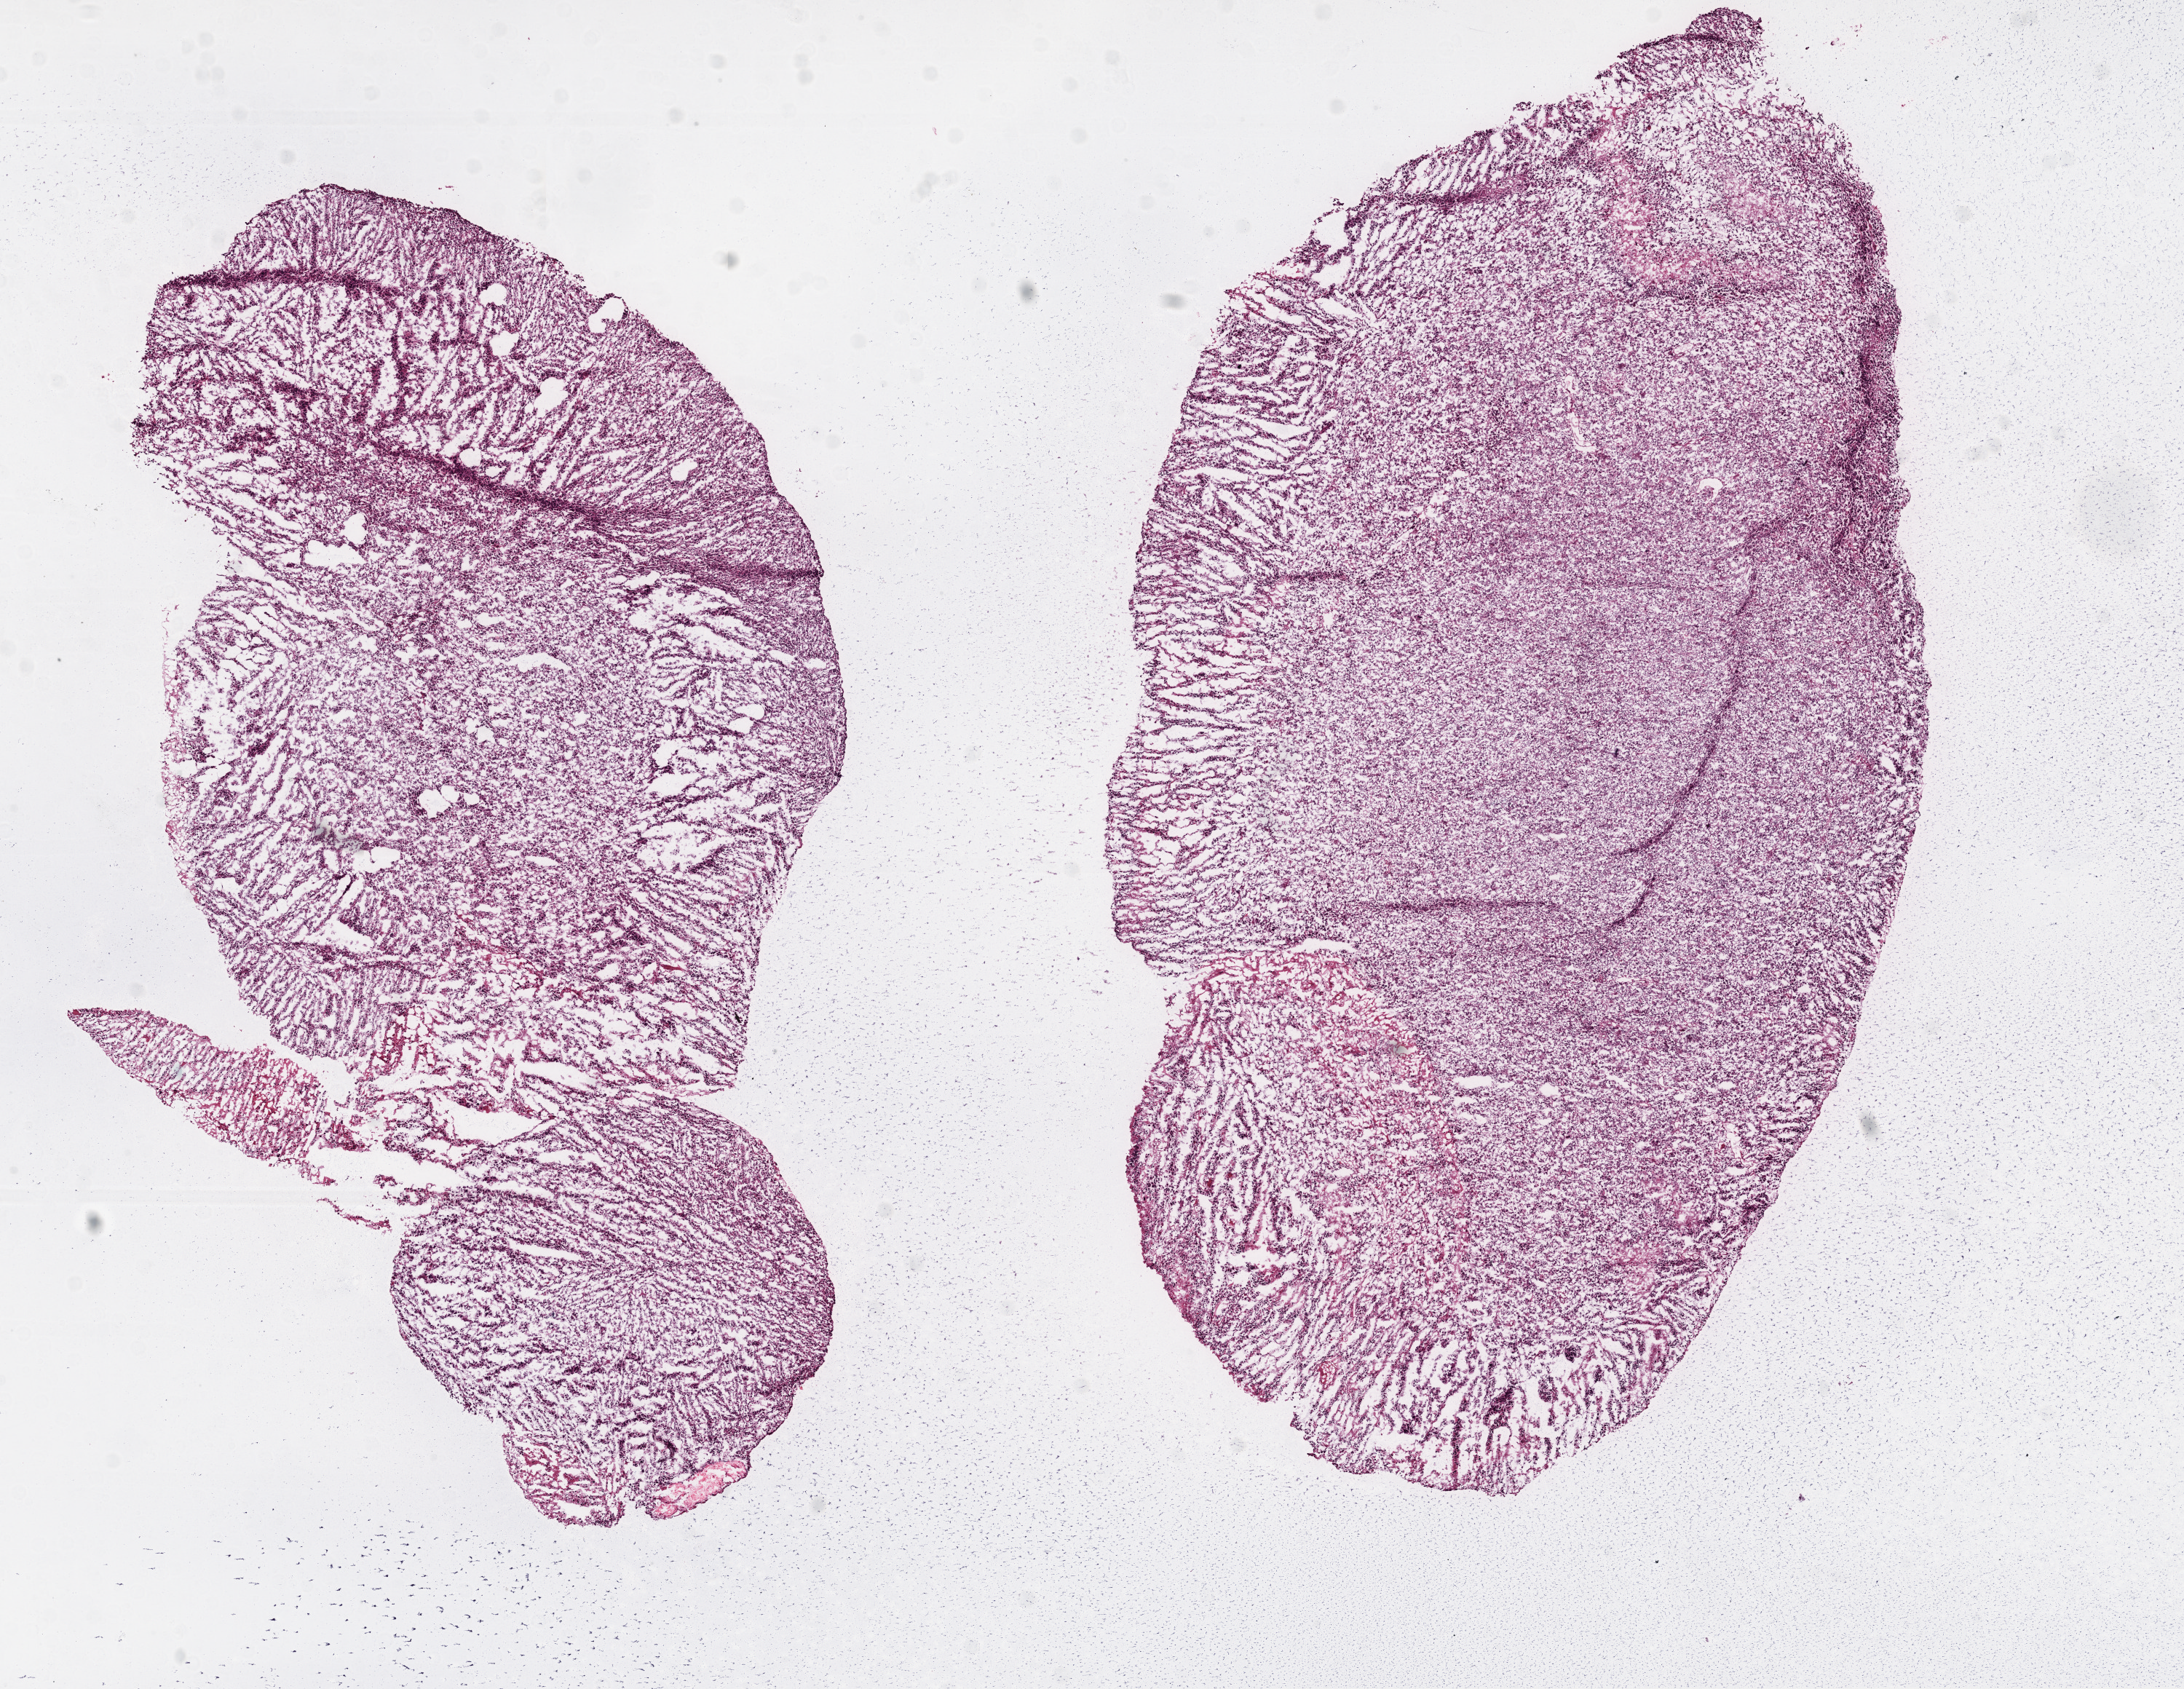
Digitized H&E tissue section (whole slide) — a low-resolution overview of the entire scanned area, about 12.0 x 9.3 mm (acquisition: 20x scan); frozen section from the top of the tissue portion; brain, primary tumour sample. Female, age 38 years at initial diagnosis. Composition of this section per pathologist review: tumour cells 85%, tumour nuclei 85%, normal cells 0%, stromal cells 0%, necrosis 15%.
Pathologic diagnosis: Glioblastoma.